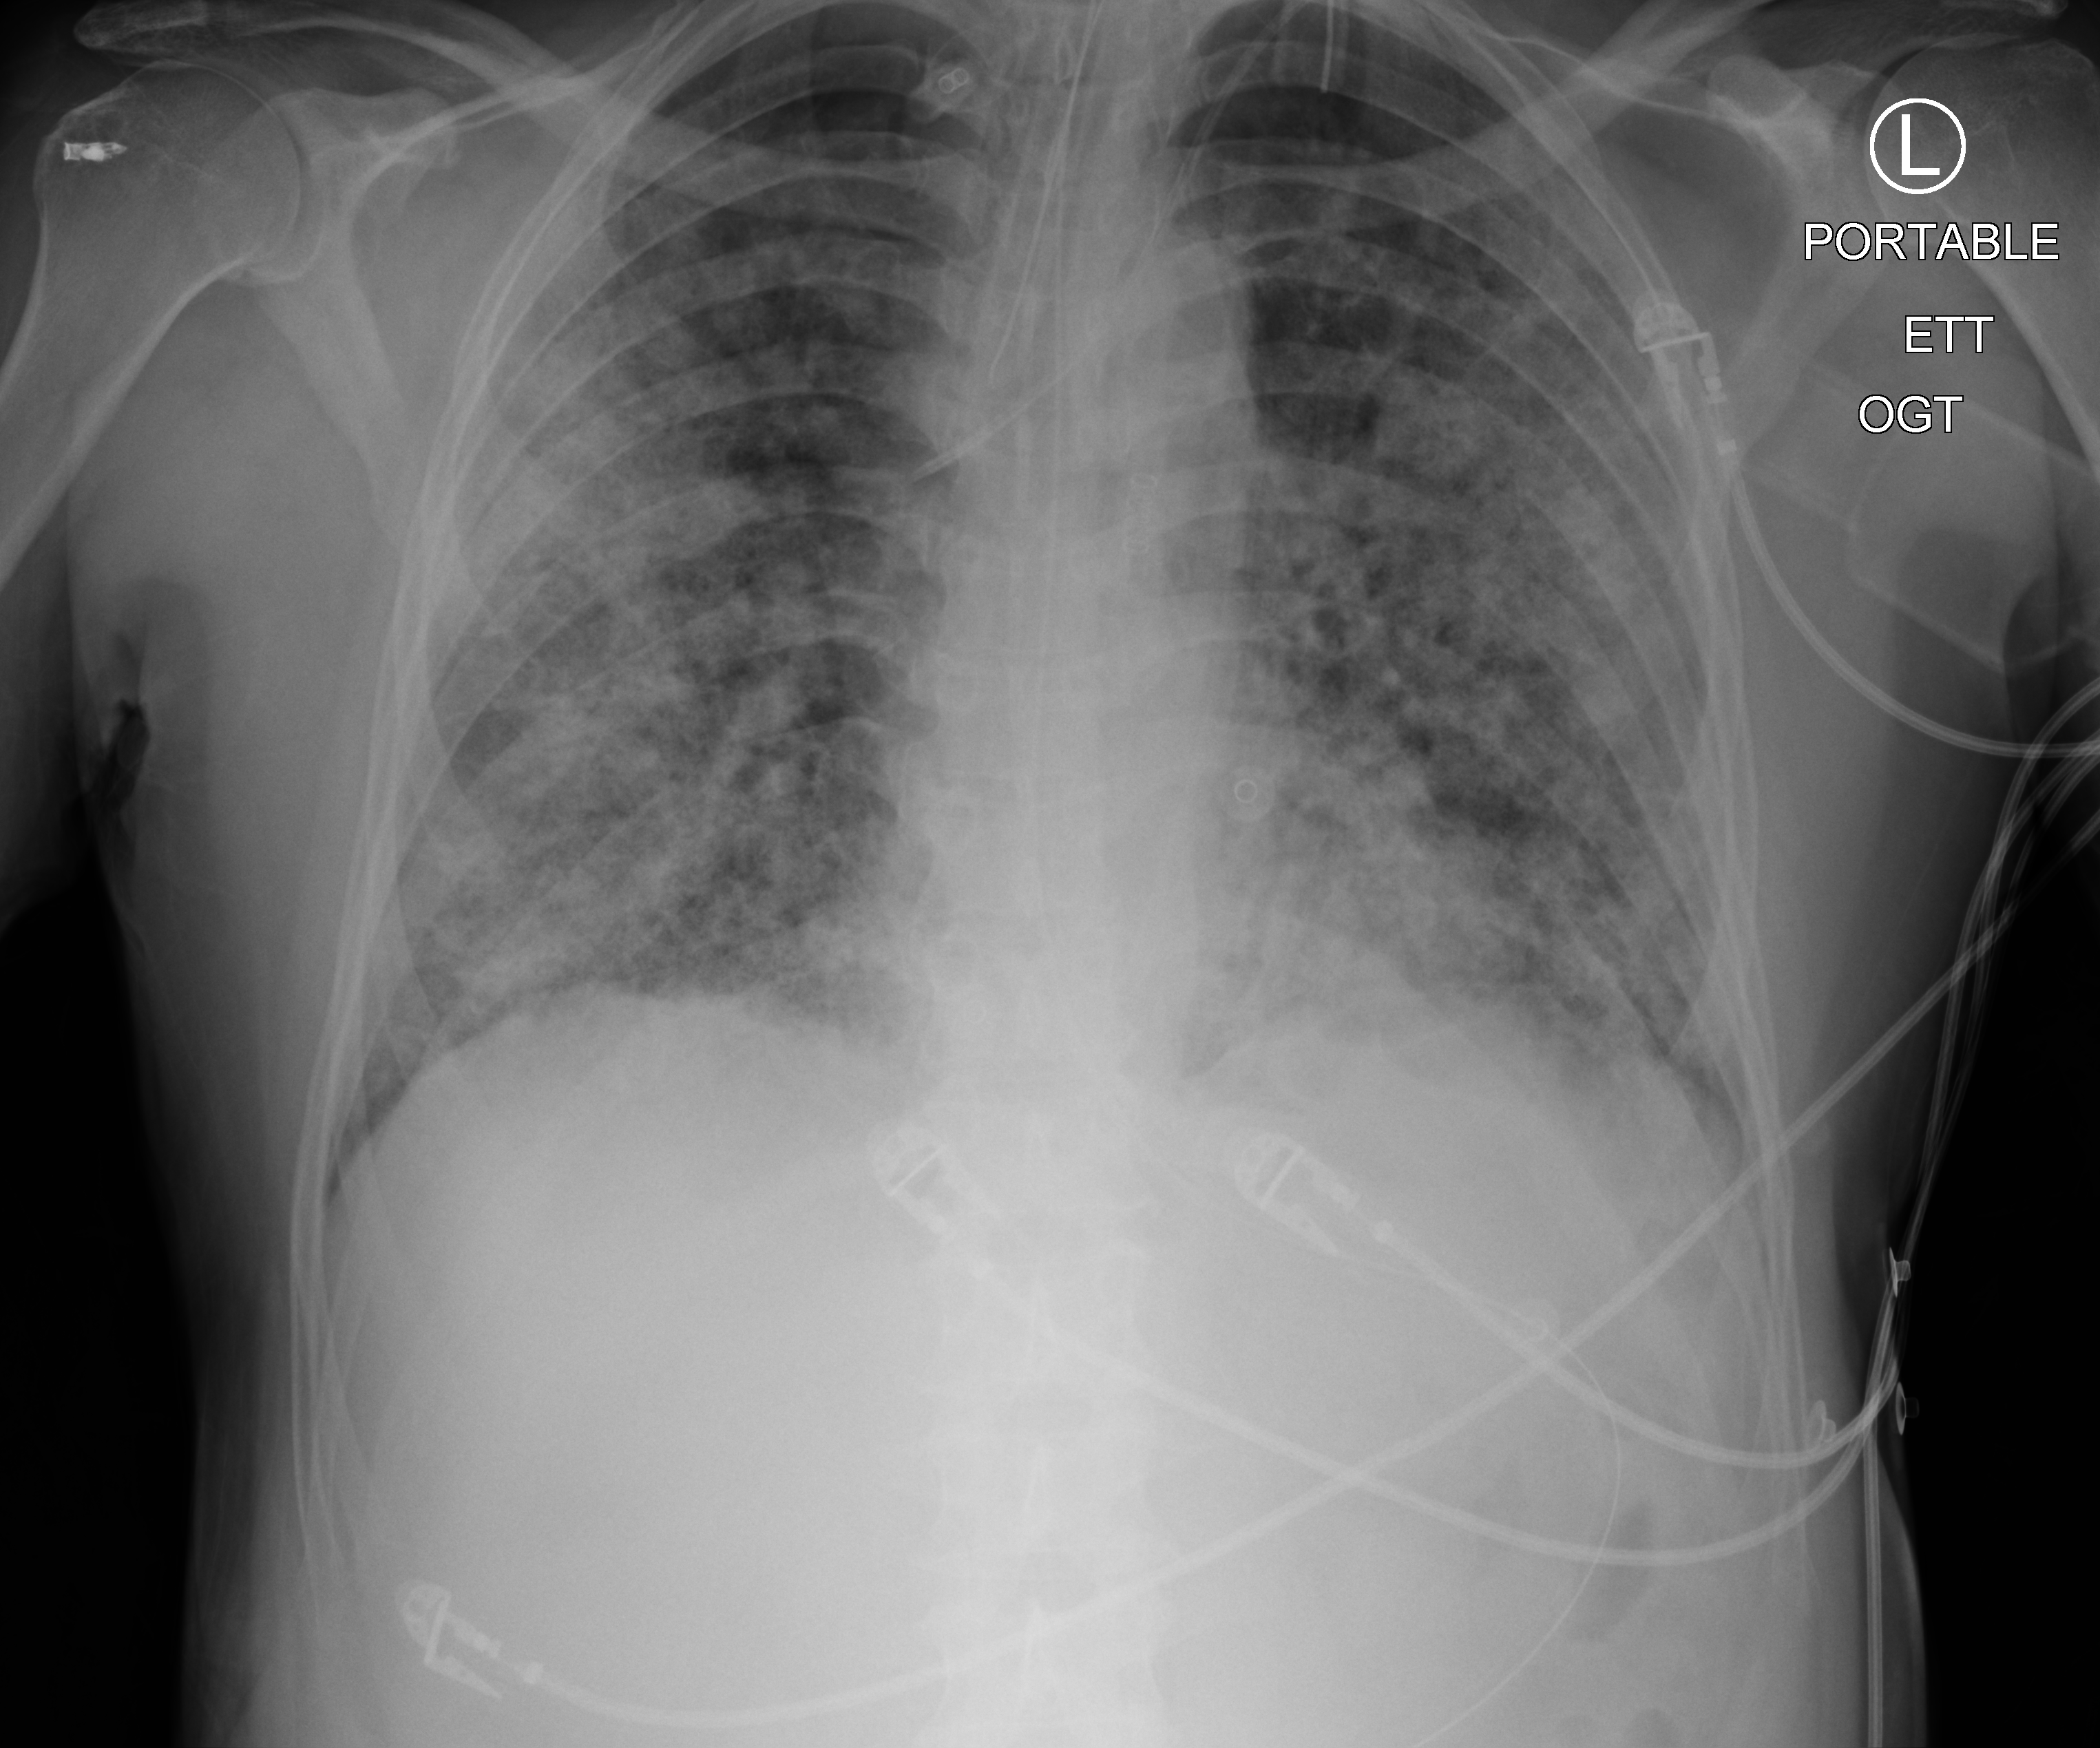
Chest X-ray (portable); anteroposterior (AP) projection. Patient hospitalised with COVID-19; male, aged 60–74 years.
From the hospital-stay record, not from the radiograph (when in the stay this image was taken is not recorded):
- smoking status (admission record): never
- chronic kidney disease (admission record): no